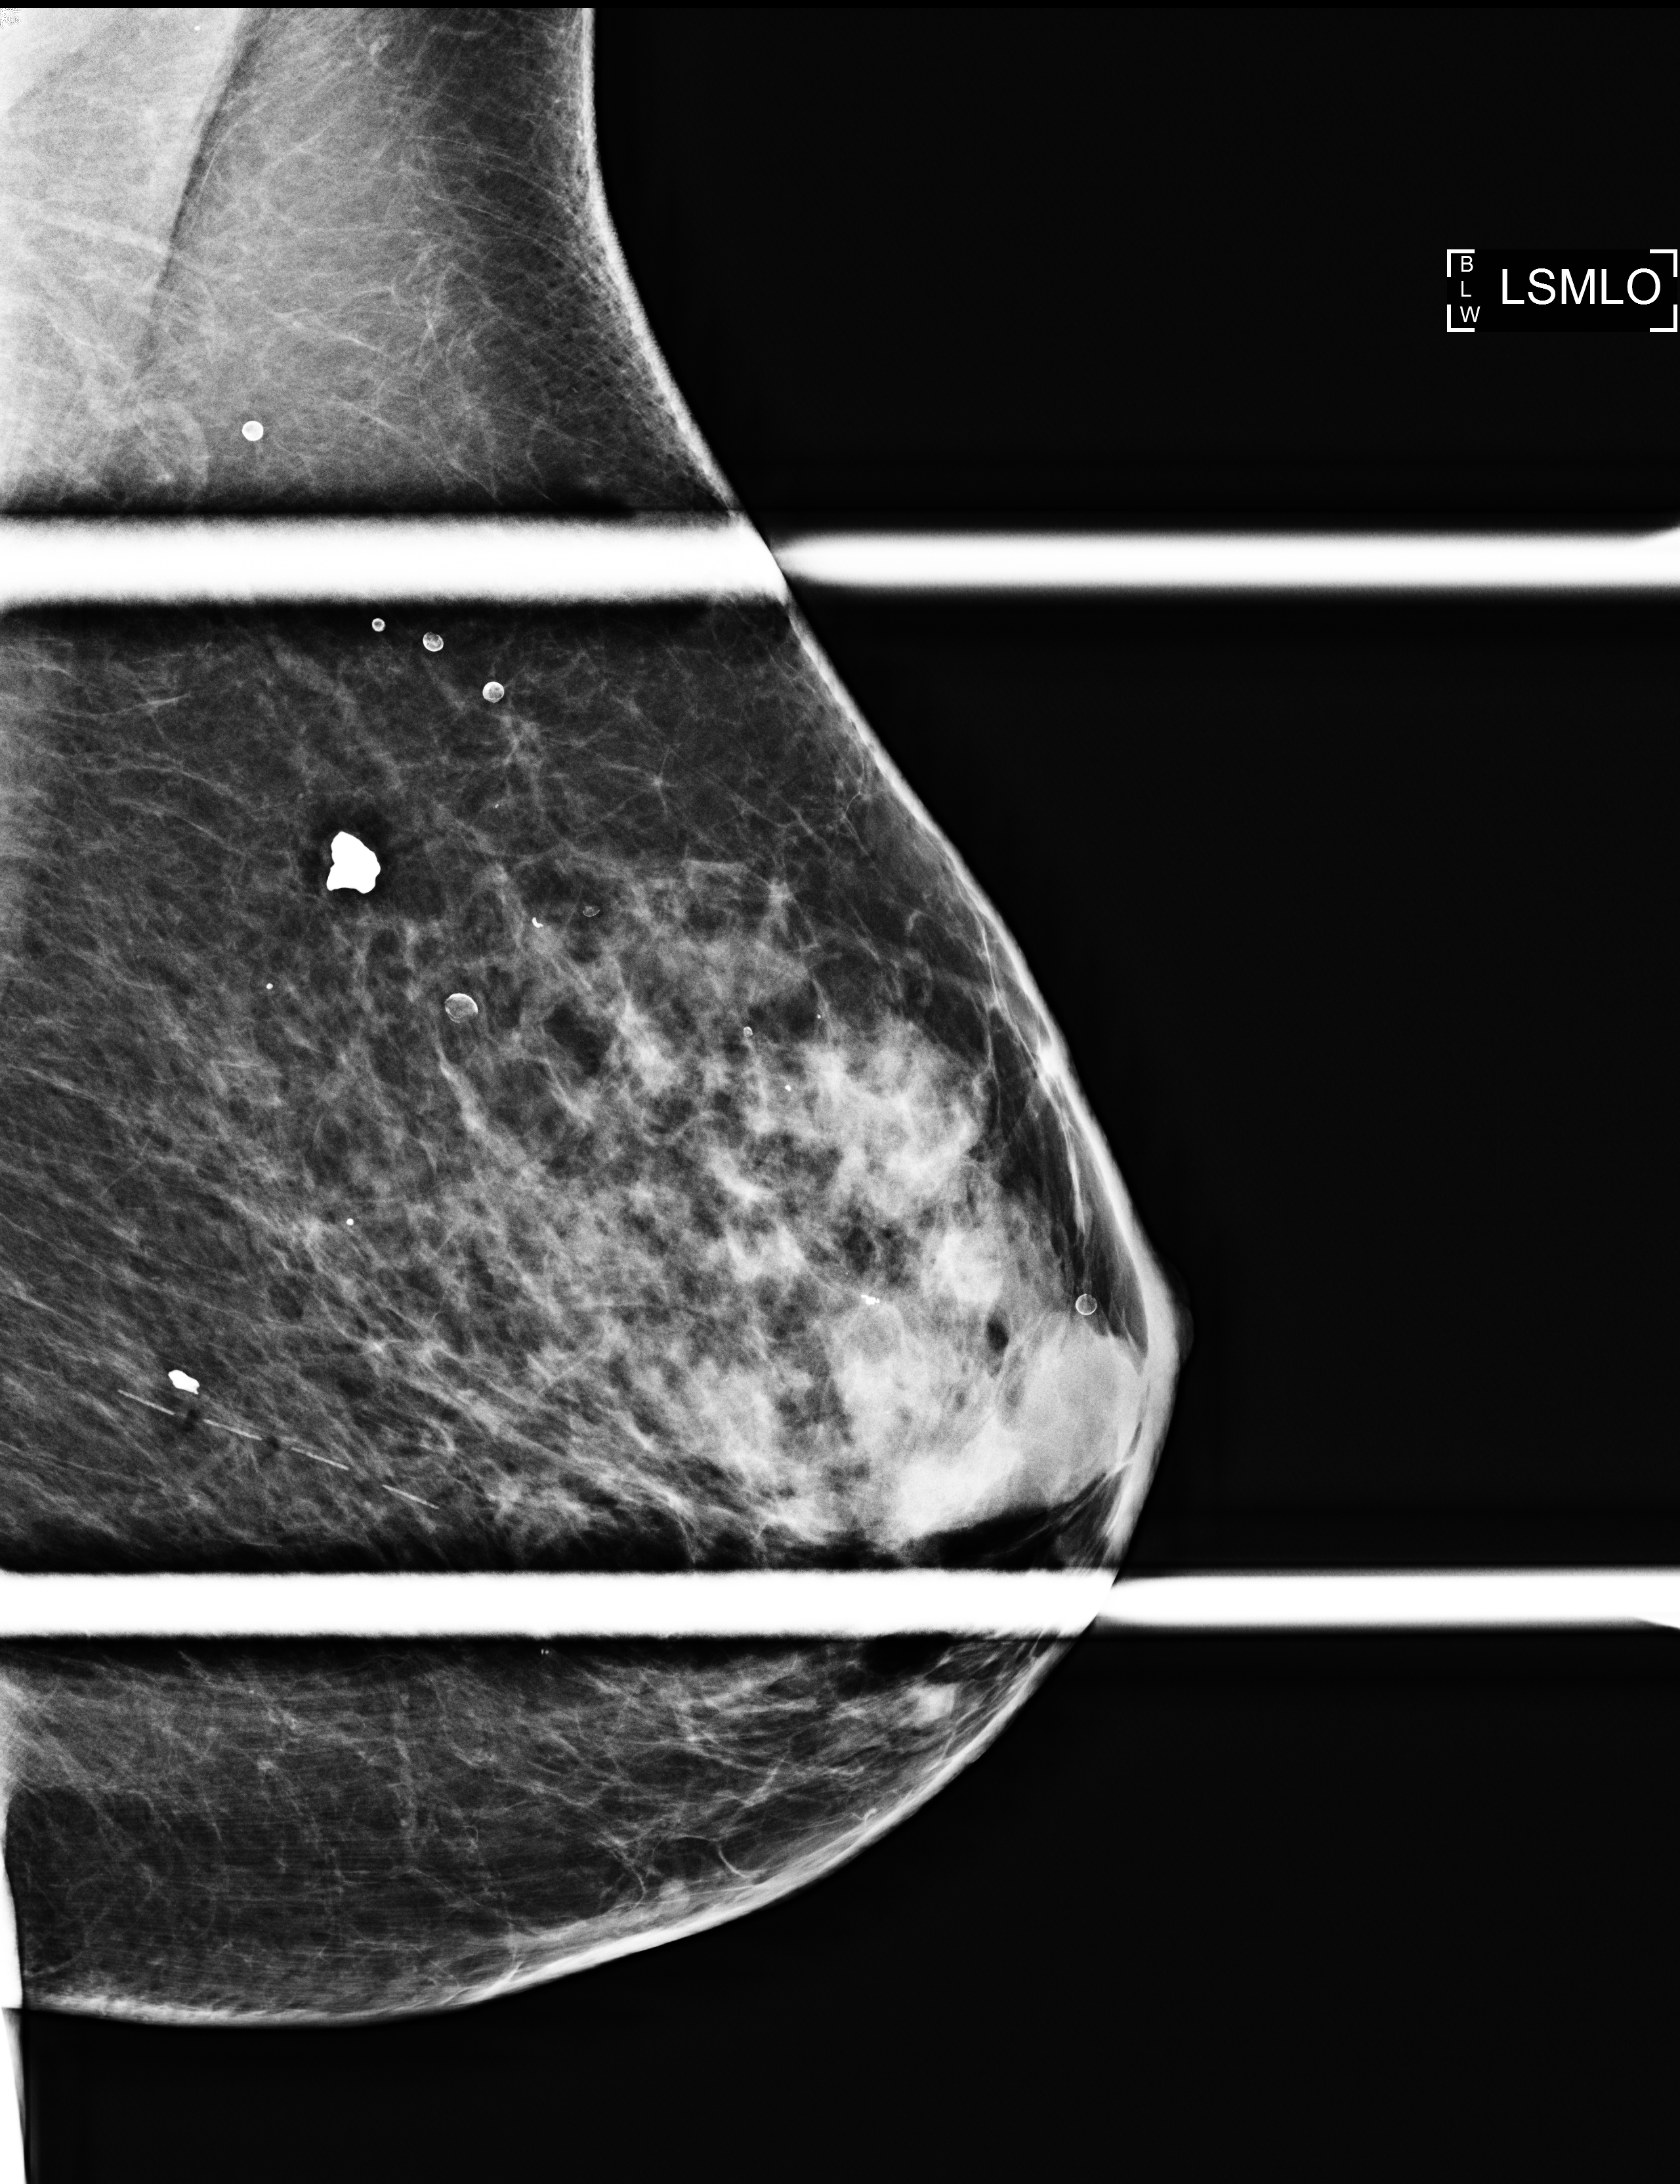
Additional (diagnostic) view. Patient: female, 69 years.
Image type: full-field digital mammogram. Breast: left. Projection: medio-lateral oblique projection, spot compression.